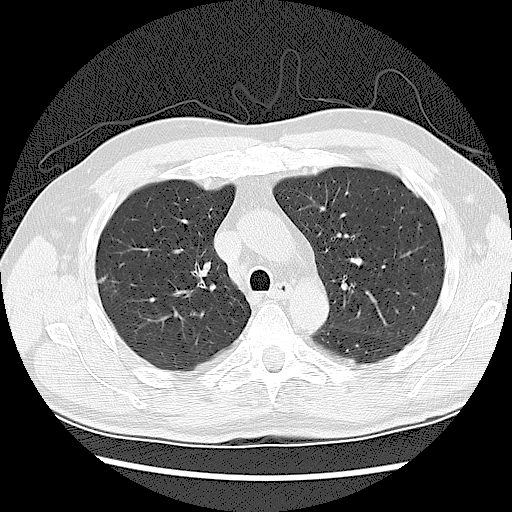
Low-dose screening chest CT, axial slice. Second annual screen. Lung window (W 1500 / L -600 HU). 2.5 mm slice thickness. Slice 38 of 120 in the series. Male, age 62 years at enrolment.
Expert-annotated lung lesion, bounding box [x1, y1, x2, y2] px = [88, 269, 118, 296]. The exam's reader record, not a measurement of the box and not confirmed to be the same lesion: non-calcified nodule or mass ≥4 mm, right upper lobe, 10 × 10 mm, smooth margins, soft tissue attenuation, pre-existing on the prior screen: yes; interval growth: yes. Official screen result: positive, other. Participant outcome: lung cancer diagnosed 6 days after this screen — adenocarcinoma, NOS, right upper lobe, poorly differentiated (G3), stage IIB (AJCC 6th edition), 5 mm at pathology.